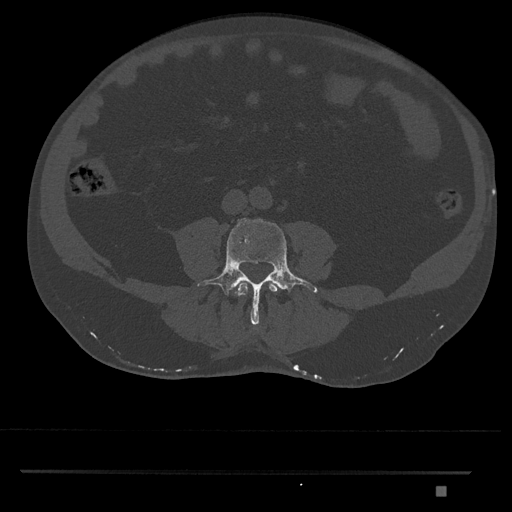
CT including the spine, one axial slice; position 628 of 1134 along the scan axis; 120 kVp; bone window (W 1800 / L 400 HU); 512 × 512 image matrix. Patient: male, 65 years. From the clinical record (not read from this slice): primary cancer: prostate.
Structures marked on this image (semi-automatically segmented with operator editing):
- L3 vertebra: bounding box (x1, y1, x2, y2) in pixels: (235, 281, 279, 297)
- L4 vertebra: (197, 218, 318, 326)